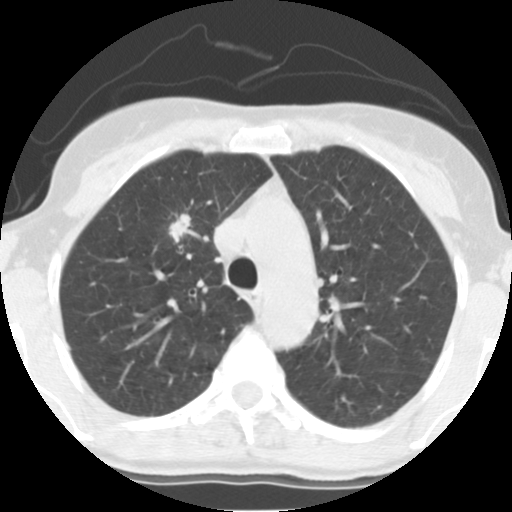
Low-dose screening chest CT, axial slice. Third screening round (two years after baseline). Lung window (W 1500 / L -600 HU). 2.5 mm slice thickness. Female participant, aged 56 years at enrolment.
Expert reader's lesion annotation, bounding box [x1, y1, x2, y2] px = [159, 209, 202, 253]. The exam's reader record, not a measurement of the box and not confirmed to be the same lesion: non-calcified nodule or mass ≥4 mm, right upper lobe, 17 × 12 mm, spiculated (stellate) margins, soft tissue attenuation, pre-existing on the prior screen: yes; interval growth: yes. Official screen result: positive, other. Later outcome: lung cancer diagnosed 49 days after this screen — adenocarcinoma, NOS, right upper lobe, moderately differentiated (G2), stage IA (AJCC 6th edition), 19 mm at pathology.